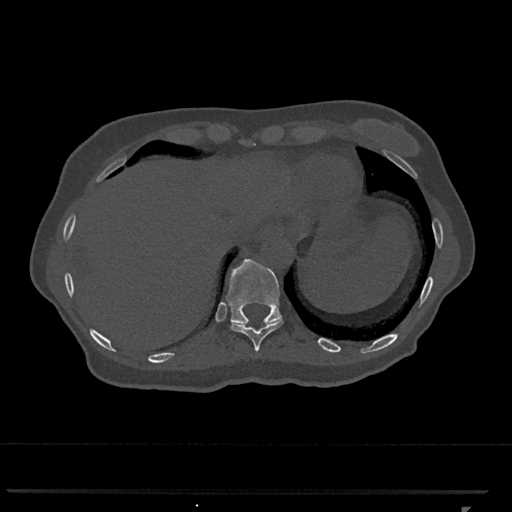
CT including the spine, one axial slice; slice 546 of 793 in the series (ordered by position); 120 kVp; bone window (W 1800 / L 400 HU); 512 × 512 image matrix, field of view 380 × 380 mm. Female patient, age 62 years. Case-level facts recorded for this patient, not image findings: primary cancer: renal.
Outlined on this slice (semi-automatic segmentation, software-assisted and operator-edited):
- T10 vertebra: bounding box [x1, y1, x2, y2] px = [230, 320, 283, 352]
- T11 vertebra: [226, 258, 282, 327]